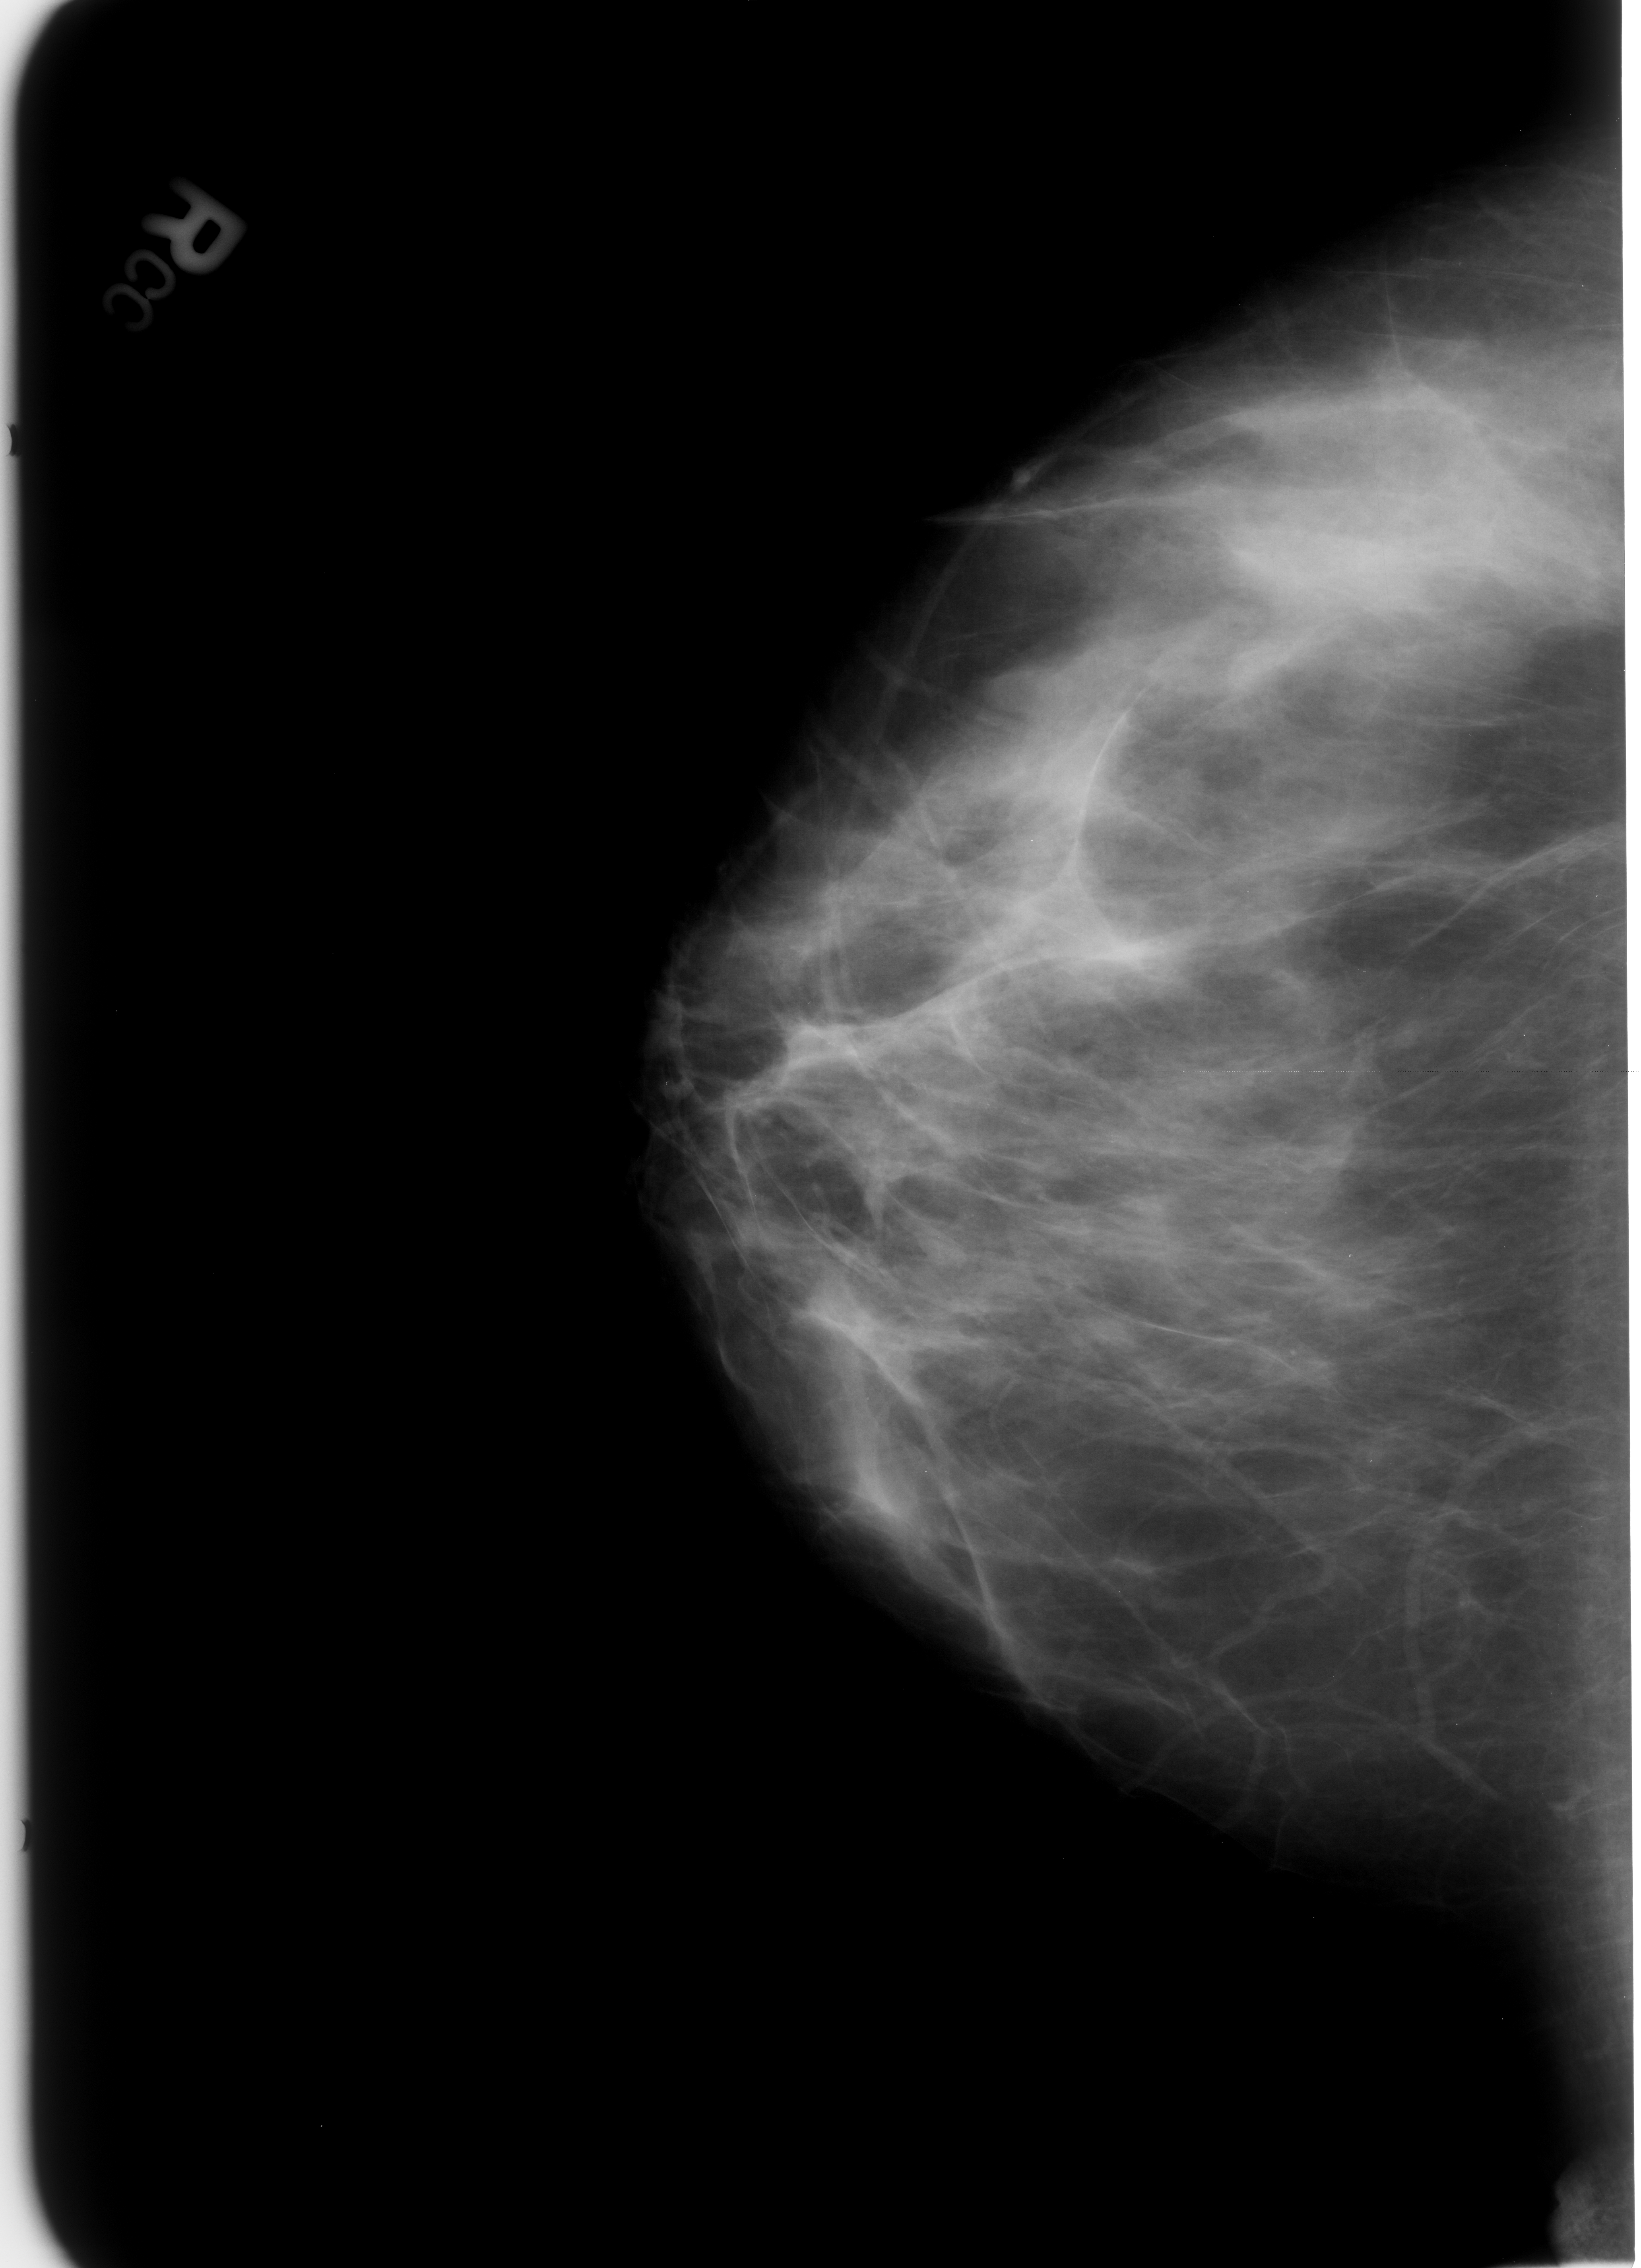
Mammogram (digitized film). Right breast. Craniocaudal (CC) view. 1641 × 2268 image matrix.
Expert-marked regions of interest on this image (one box per marked abnormality):
- calcifications, morphology vascular; BI-RADS assessment category 2; subtlety rating 3 on a 1 (subtle) to 5 (obvious) scale; benign; no additional work-up was recommended (outcome (as recorded, no biopsy): benign without callback): bounding box [x1, y1, x2, y2] px = [858, 1059, 1101, 1162]